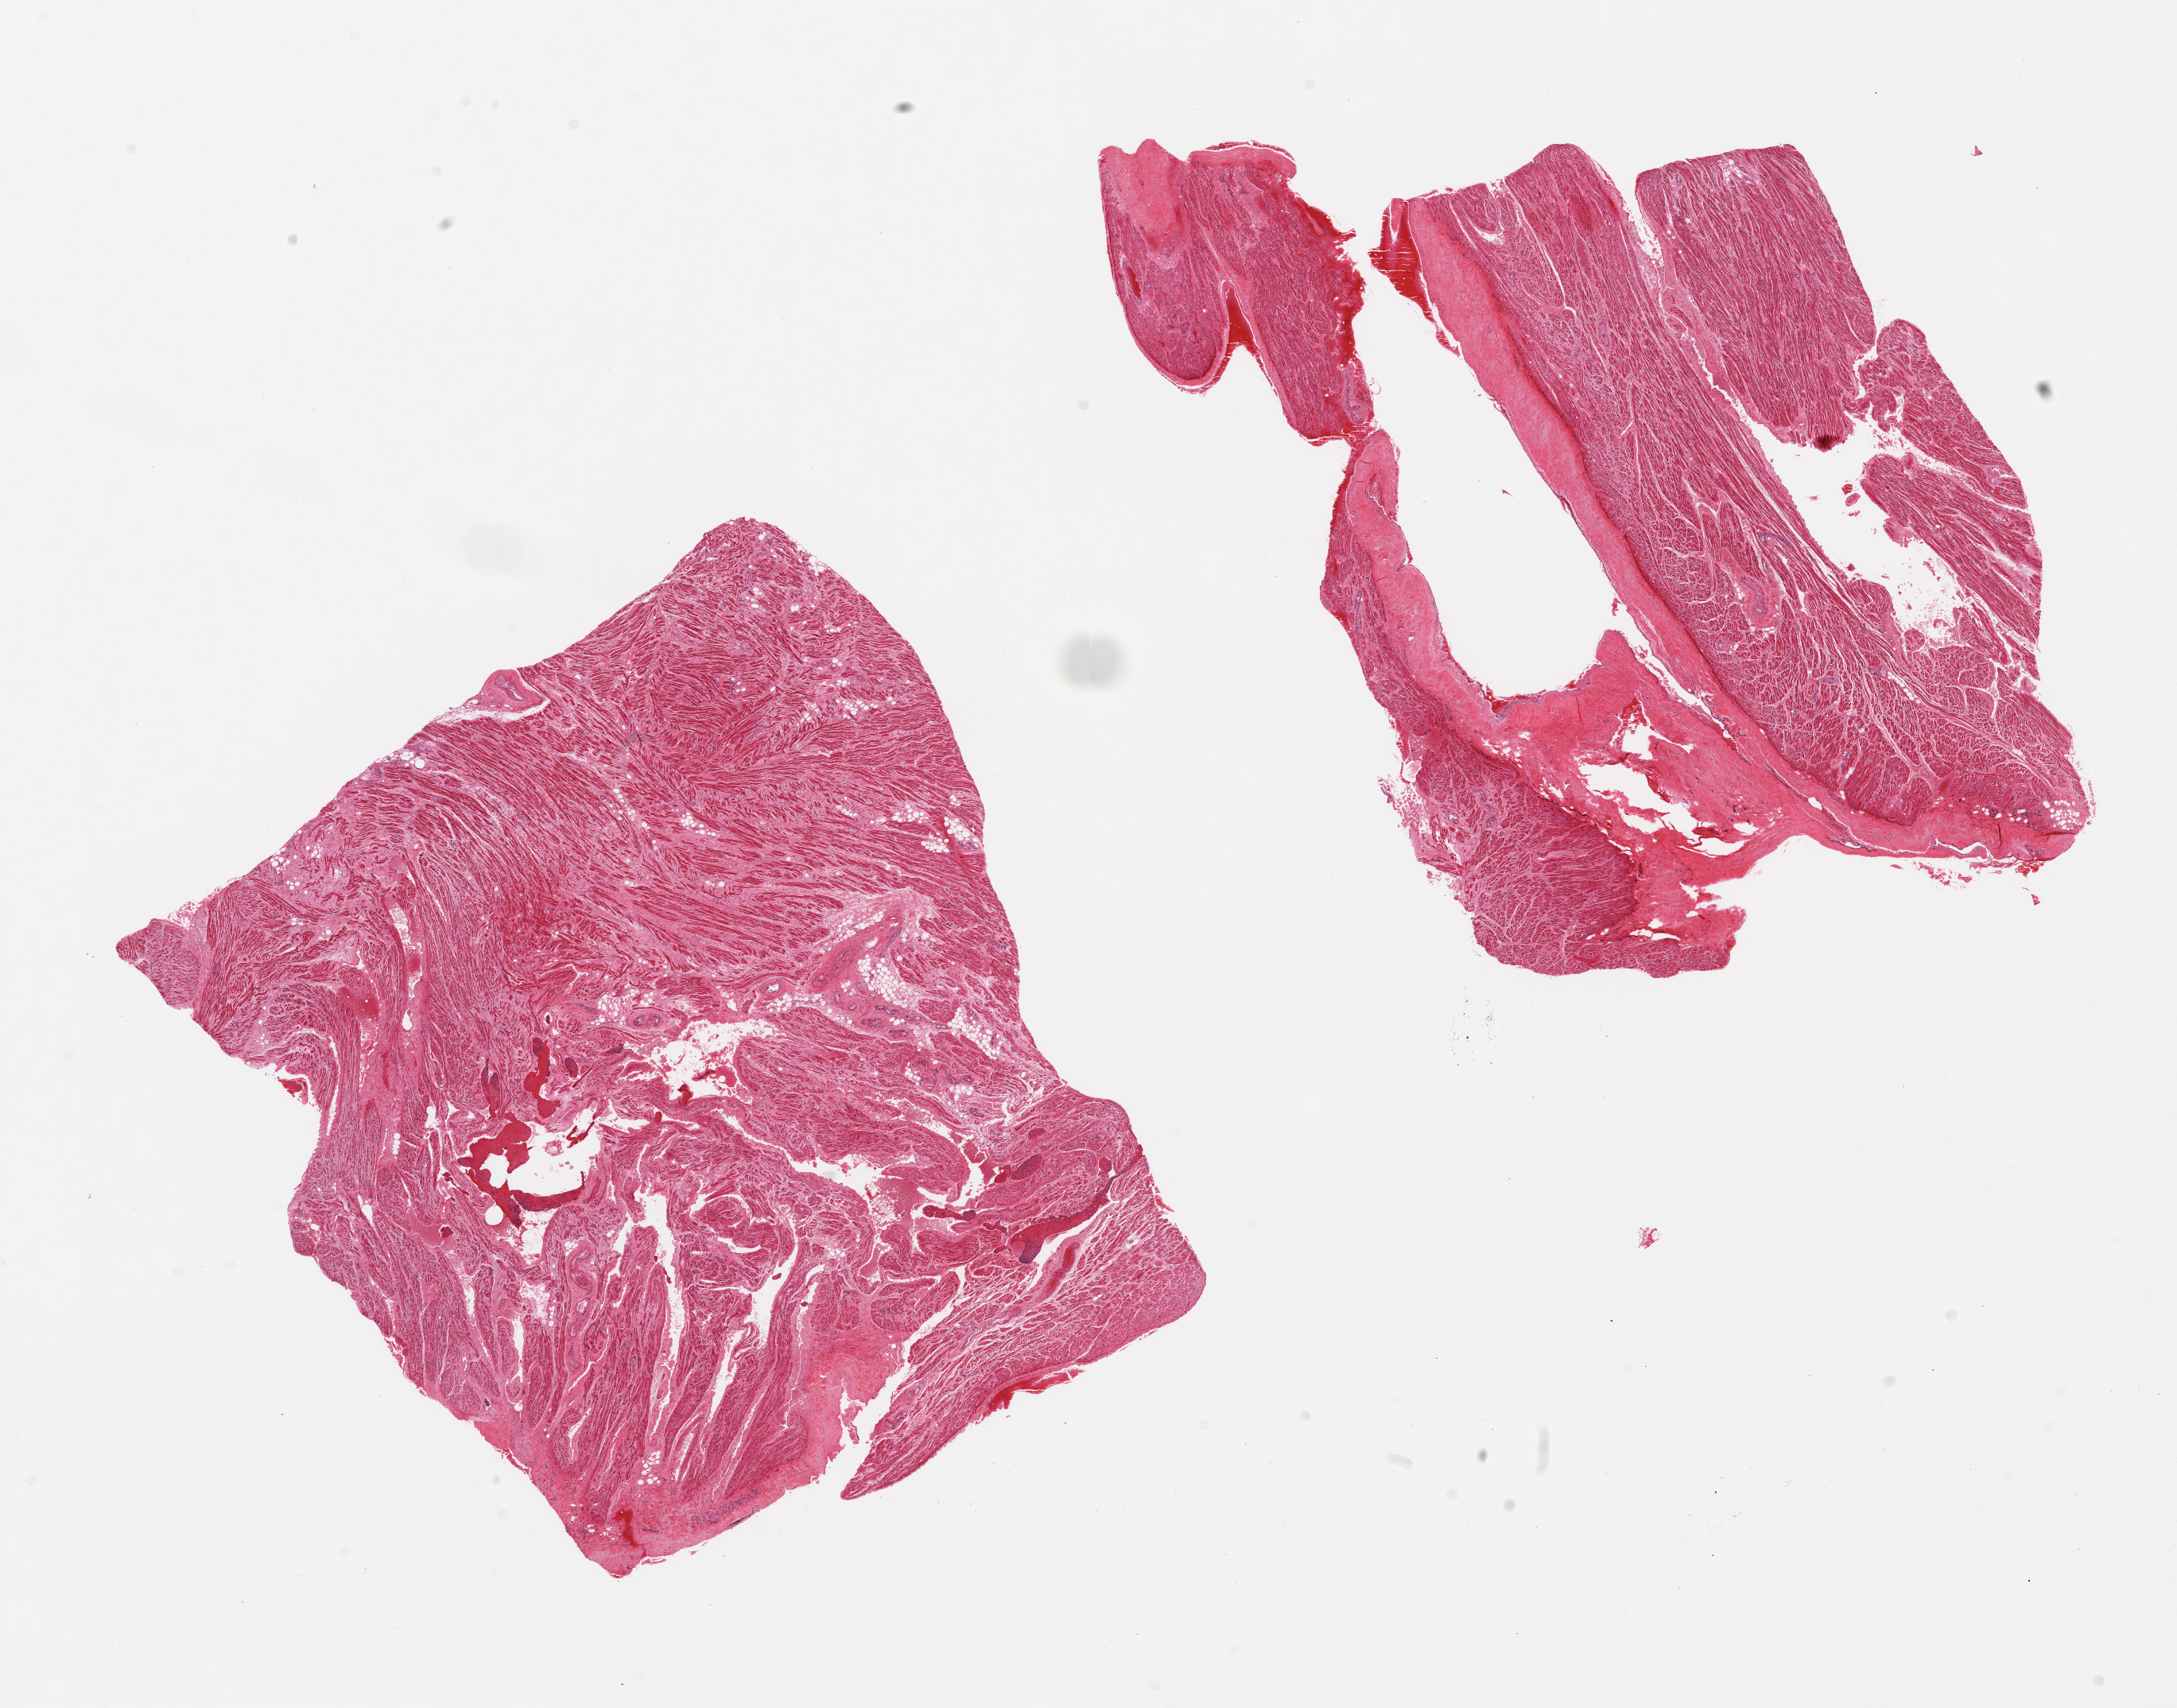
Haematoxylin and eosin whole-slide image — a low-resolution overview of the entire scanned area, about 21.7 x 17.0 mm, PAXgene-fixed paraffin-embedded (PFPE) section, target tissue: auricular appendage, tissue donor sample.
• pathologist's review note for this sample: 2 pieces, no abnormalities